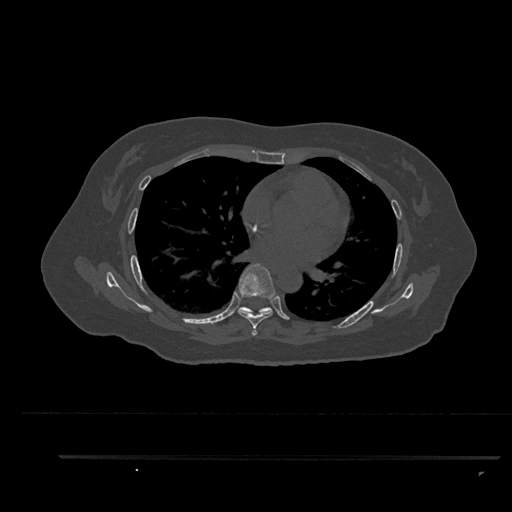
CT including the spine, one axial slice; slice 541 of 797 in the series (ordered by position); bone window (W 1800 / L 400 HU); 0.5 mm slice thickness; 512 × 512 image matrix, field of view 408 × 408 mm. Female patient, age 44 years. Case-level facts recorded for this patient, not image findings: primary cancer: renal; vertebrae with lytic lesions (as recorded): L1.
Outlined on this slice (semi-automatic segmentation, software-assisted and operator-edited):
- T6 vertebra: bounding box (x1, y1, x2, y2) in pixels: (238, 263, 276, 336)
- T7 vertebra: (238, 307, 272, 315)